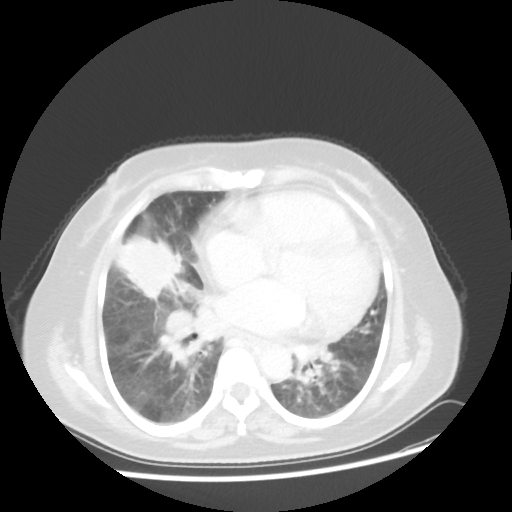
Chest CT, one axial slice; slice 20 of 45 in the series (ordered by position); reconstruction kernel STANDARD; 100 kVp; lung window (W 1500 / L -600 HU); 512 × 512 image matrix, field of view 359 × 359 mm. Patient: female, 67 years. Case-level facts recorded for this patient, not image findings: clinical TNM (as recorded): T2a N3 M1a.
Annotated regions visible in this slice (bounding box drawn by a radiologist):
- lung tumour (recorded histology: adenocarcinoma): bounding box [x1, y1, x2, y2] px = [118, 232, 184, 302]